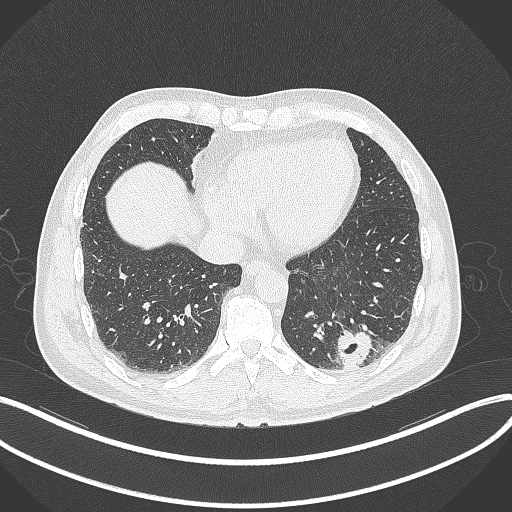
Chest CT, one axial slice; position 80 of 300 along the scan axis; lung window (W 1500 / L -600 HU); 1 mm slice thickness; 512 × 512 image matrix, field of view 400 × 400 mm. Patient: male, 54 years. Case-level facts recorded for this patient, not image findings: clinical TNM (as recorded): T1c N0 M1.
Structures marked on this image (rectangle marked by the reading radiologist):
- lung tumour (recorded histology: adenocarcinoma): bounding box (x1, y1, x2, y2) in pixels: (337, 328, 372, 369)